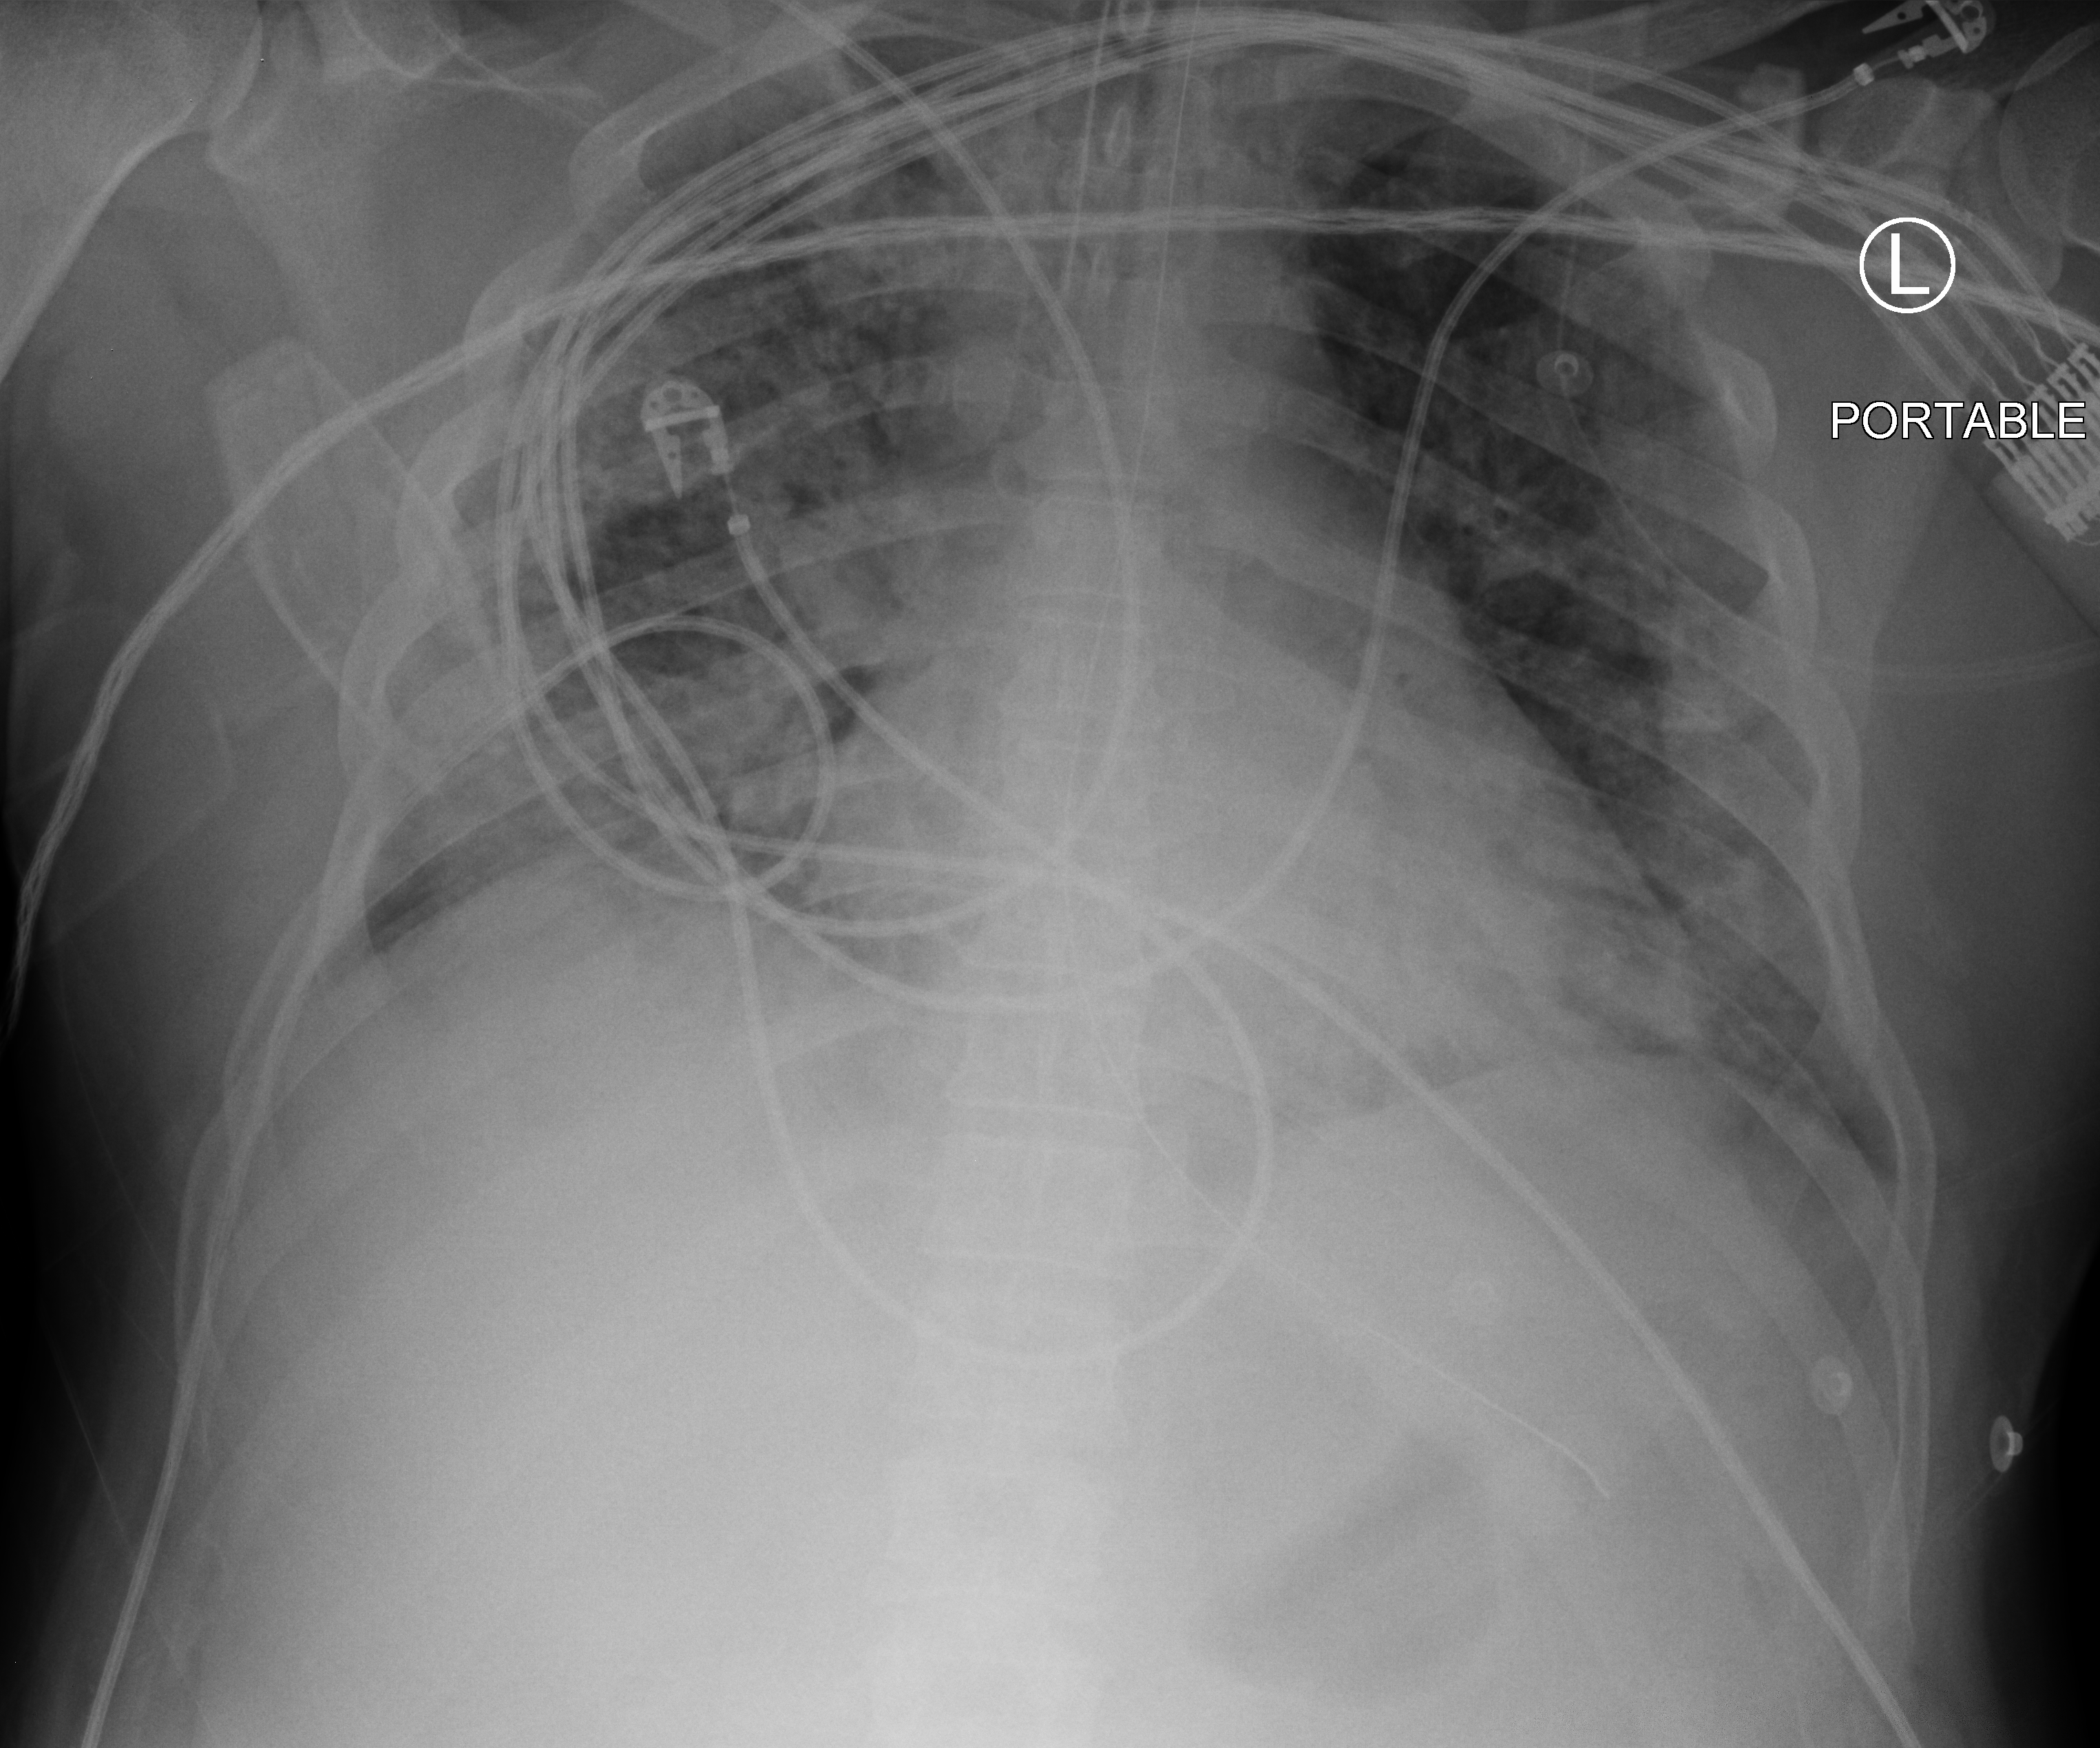
Chest X-ray (portable), anteroposterior (AP) projection. Patient hospitalised with COVID-19; male, aged 18–59 years.
Admission-level facts for this patient (not findings on this image; timing relative to this image not recorded): mechanically ventilated during this hospital stay: yes; length of hospital stay: 26 days; hypertension (admission record): no.